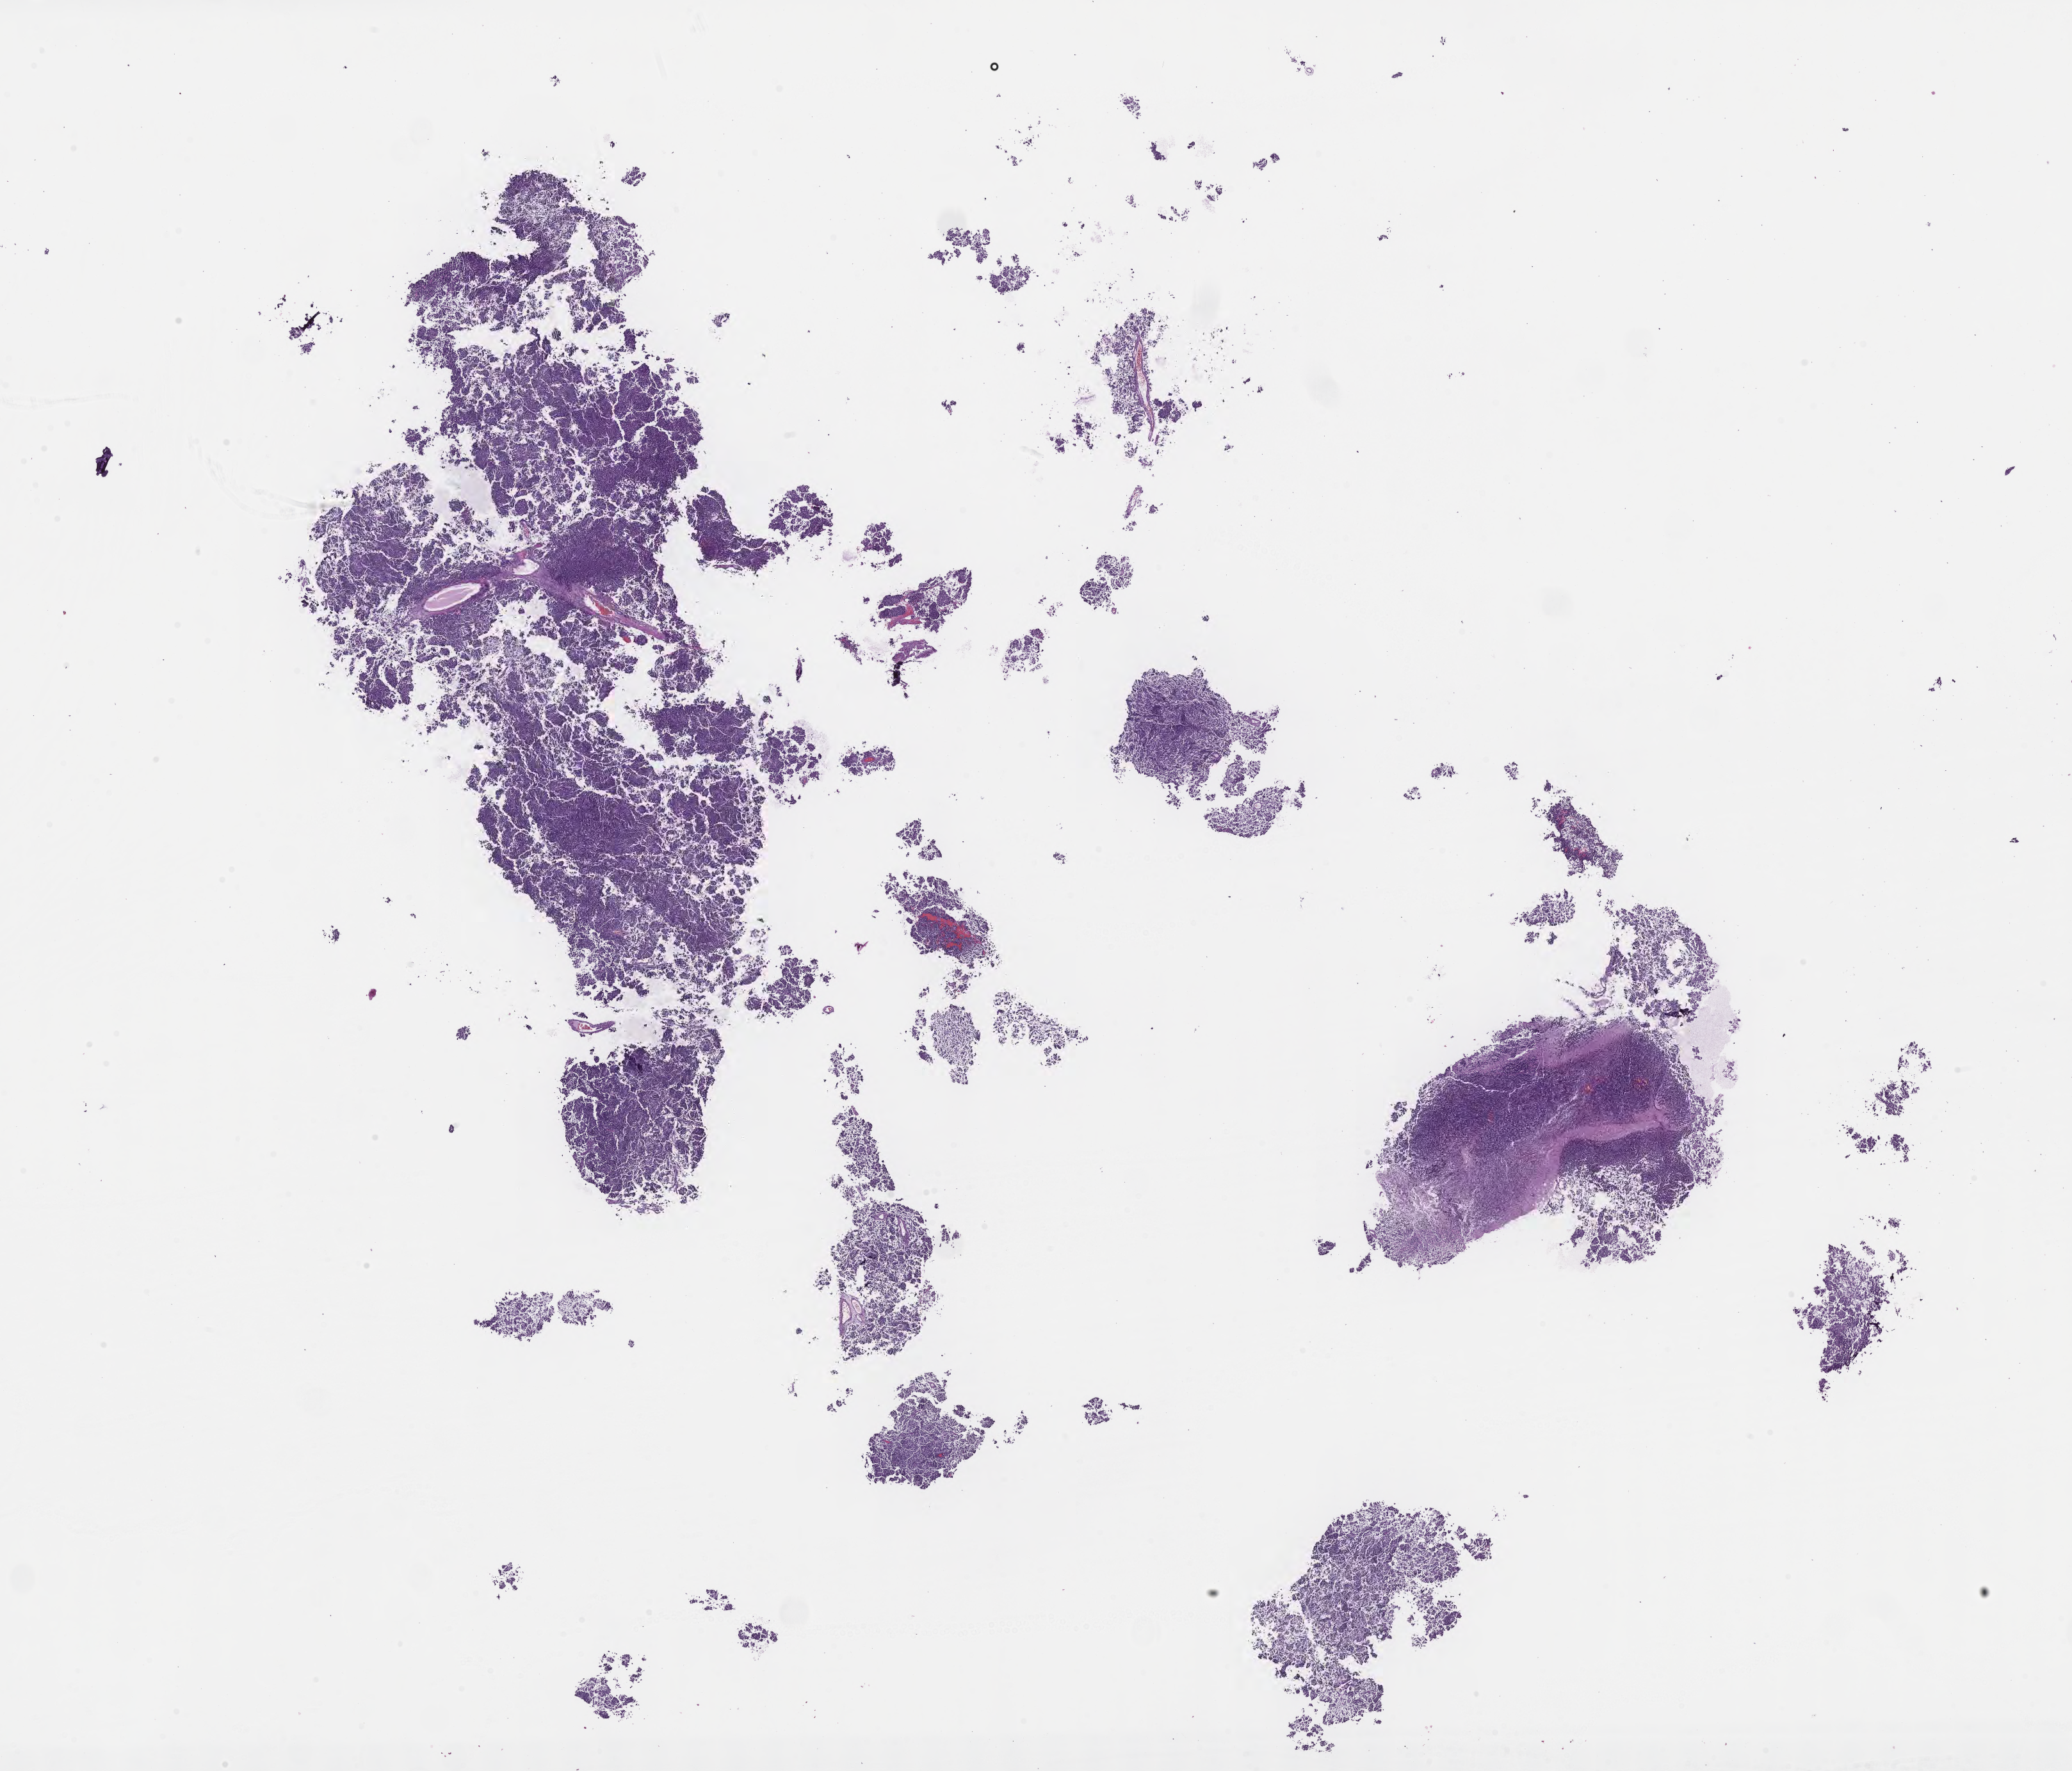
Whole-slide image, hematoxylin and eosin (H&E) stain of tumor tissue from the cerebellum — shown as a low-resolution overview of the whole scanned area (about 26.2 x 22.4 mm). Formalin-fixed, paraffin-embedded (FFPE) tissue. Patient: female, age 154 months (12 years 10 months).
Recorded diagnosis: Medulloblastoma, NOS.